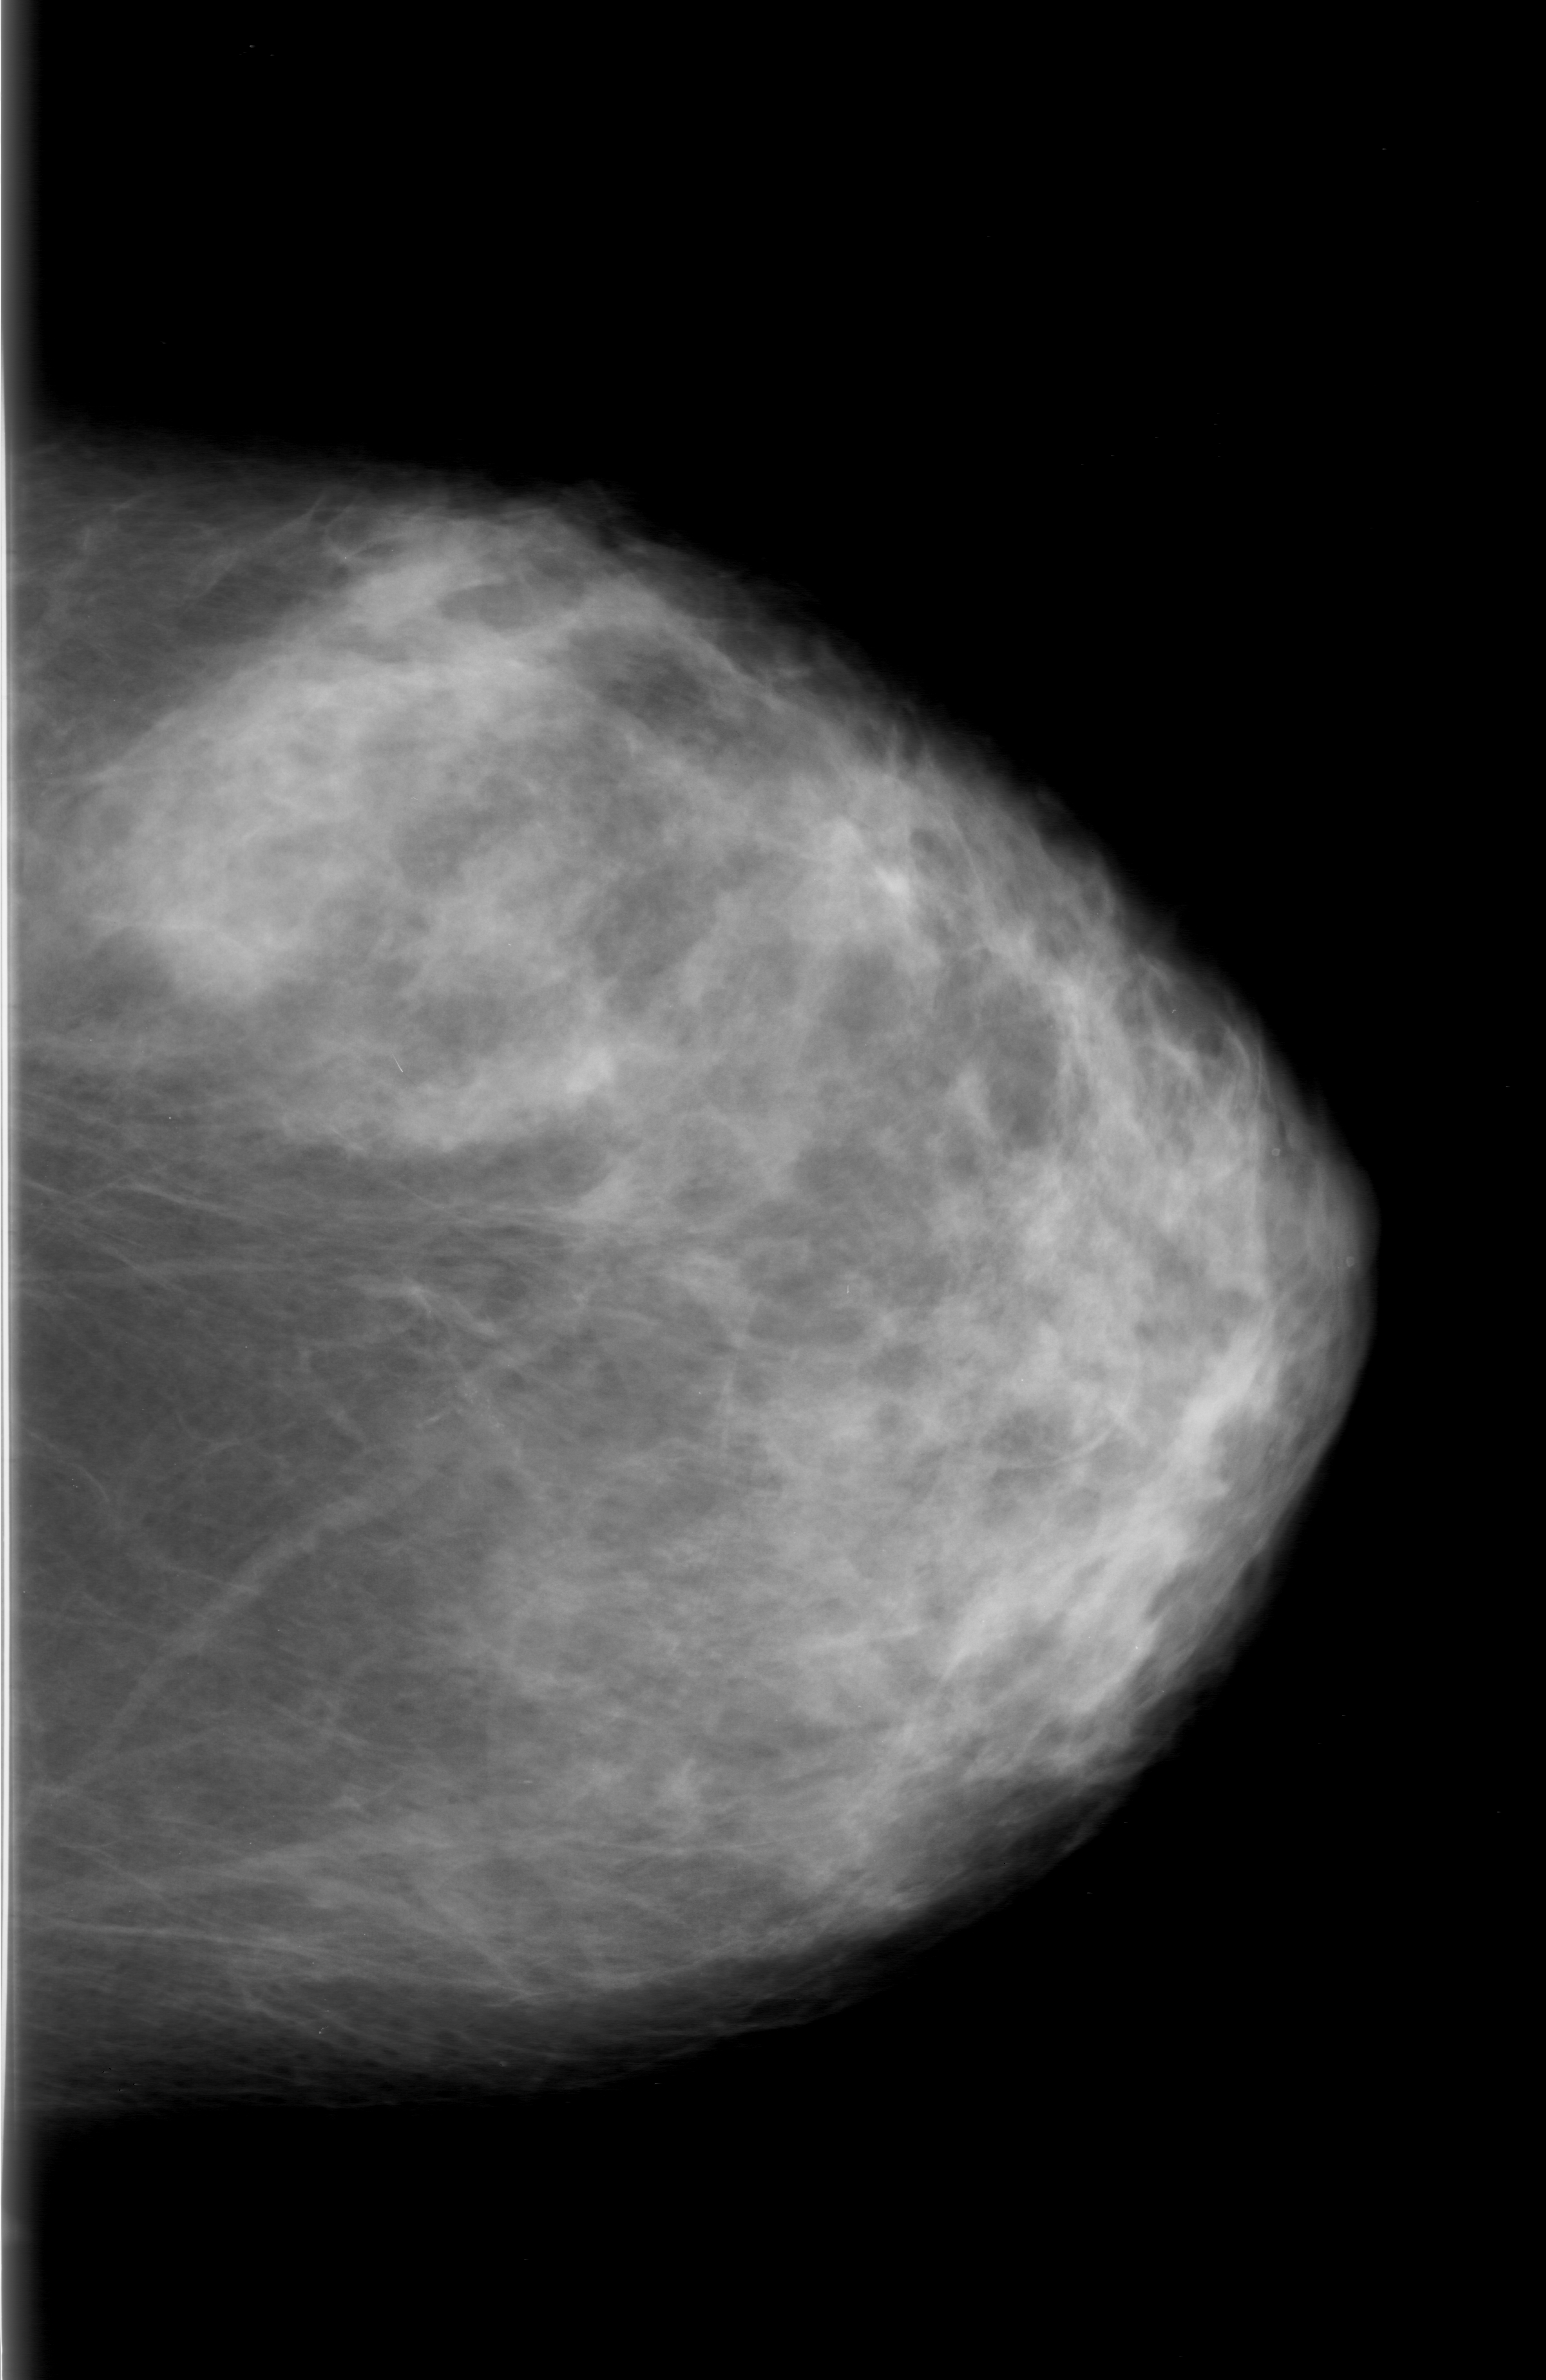
Digitized screen-film mammogram, left breast, craniocaudal (CC) view, breast composition: heterogeneously dense (BI-RADS density category 3 of 4).
- Abnormality record for this image: calcifications, morphology punctate / fine linear branching, distribution clustered; BI-RADS assessment category 0 (incomplete: needs additional imaging); subtlety rating 4 on a 1 (subtle) to 5 (obvious) scale; pathology (as recorded): malignant.